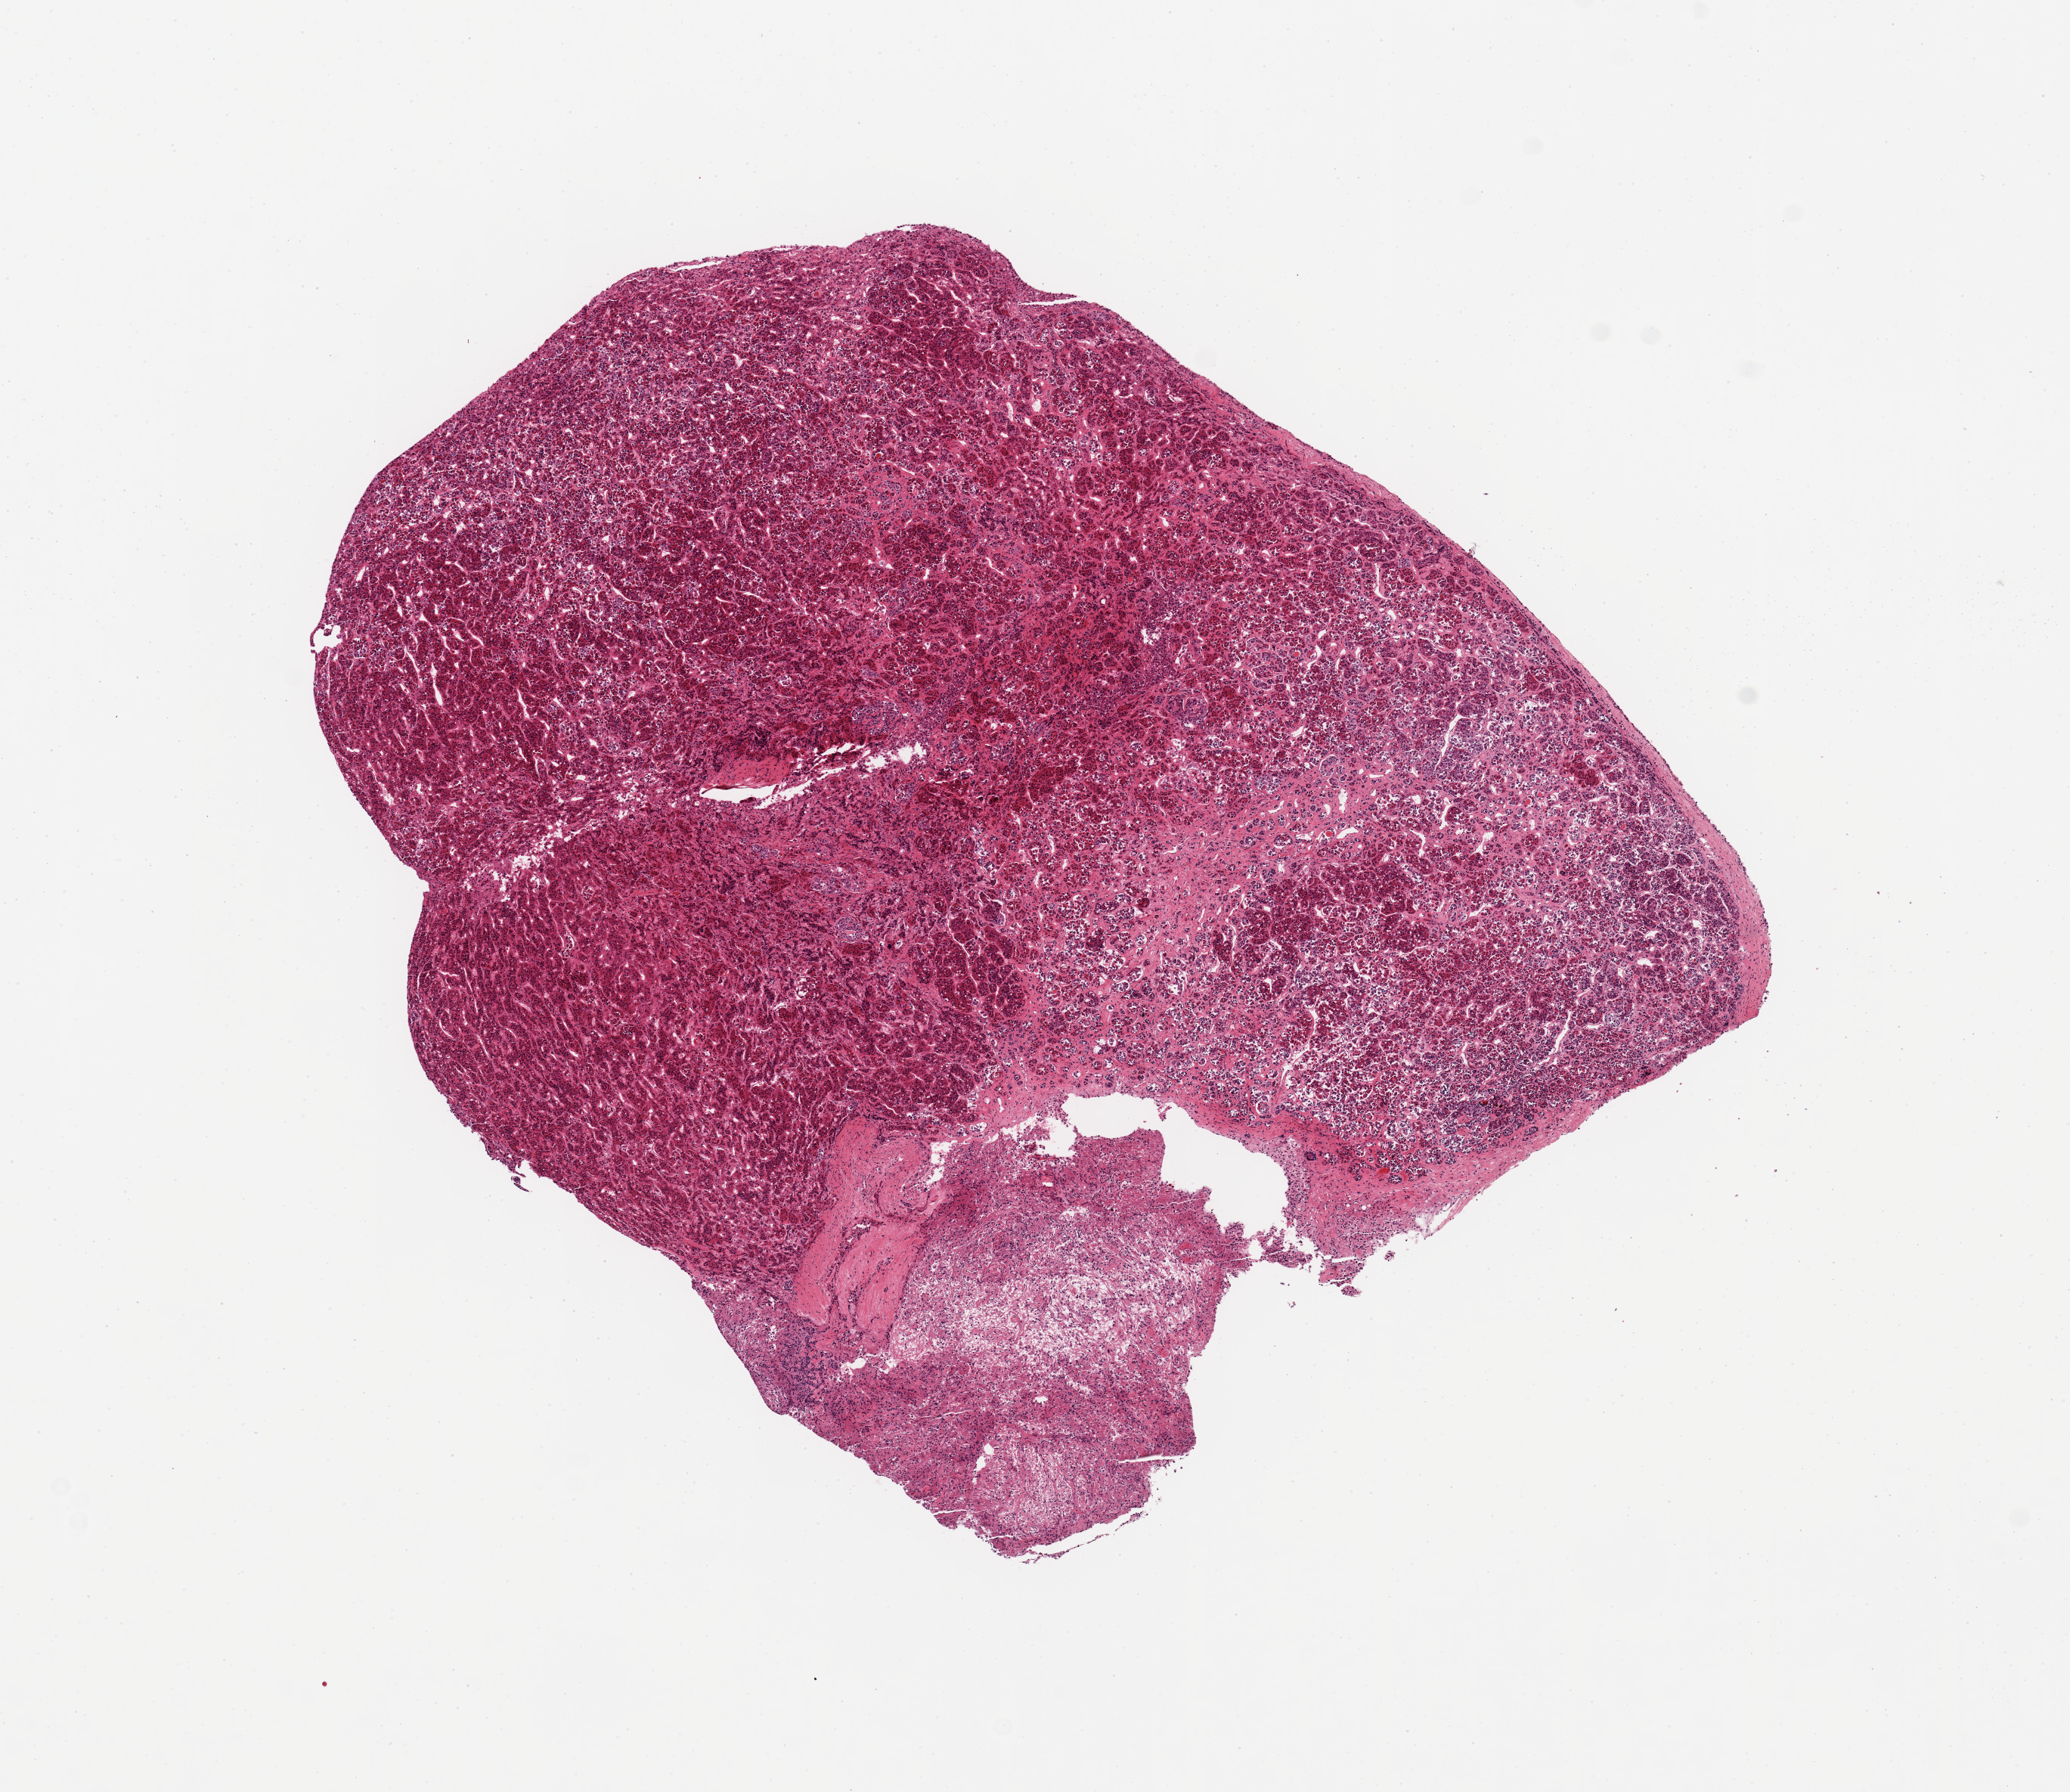
Whole-slide image, hematoxylin and eosin (H&E) stain, brightfield, low-resolution overview of the scanned area, about 10.8 x 9.4 mm, PAXgene-fixed paraffin-embedded (PFPE) section, sampled site (target tissue): pituitary, donor tissue sample. Donor: male.
* review note (as recorded): 1 piece, largely adenohypophysis; ~2.5mm nodule of neurohypophysis